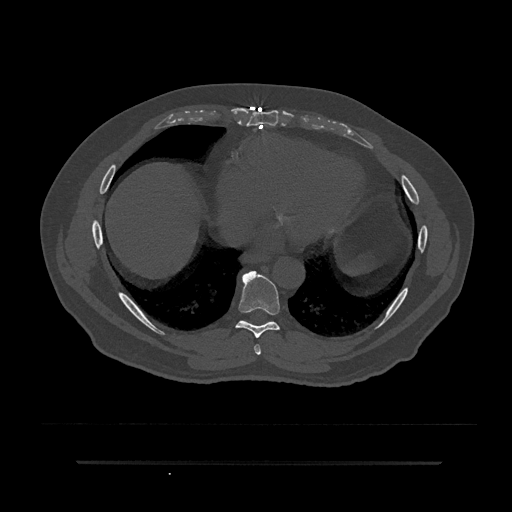
CT including the spine, one axial slice; position 422 of 797 along the scan axis; reconstruction kernel Br40s/3; bone window (W 1800 / L 400 HU); 0.5 mm slice thickness; 512 × 512 image matrix, field of view 464 × 464 mm. Male patient, age 59 years. From the clinical record (not read from this slice): primary cancer: bile ducts.
Outlined on this slice (semi-automatically segmented with operator editing):
- T7 vertebra: bounding box (x1, y1, x2, y2) in pixels: (254, 344, 261, 355)
- T8 vertebra: (235, 271, 280, 338)